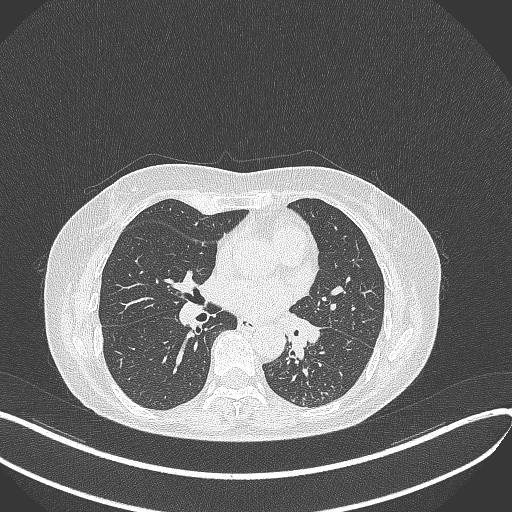
Chest CT, one axial slice. Slice 207 of 429 in the series (ordered by position). Reconstruction kernel B70f. Lung window (W 1500 / L -600 HU). 512 × 512 image matrix. Patient: female, 63 years. From the clinical record (not read from this slice): clinical TNM (as recorded): T1b N0 M0; histopathological grade: G2-3.
Annotated regions visible in this slice (rectangle marked by the reading radiologist):
- lung tumour (recorded histology: adenocarcinoma): bounding box [x1, y1, x2, y2] px = [286, 313, 323, 360]